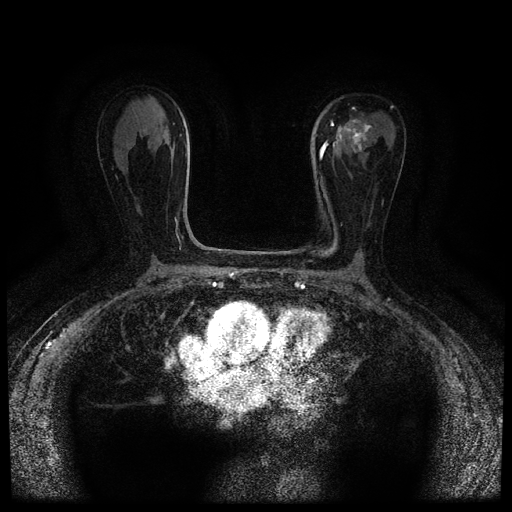
Breast MRI (dynamic contrast-enhanced, multi-phase), one axial slice. Position 45 of 116 along the scan axis. Dynamic contrast-enhanced series, time point 2 of 5 at this slice position (early post-contrast). 1.5 T. TE 2.7 ms, TR 5.4 ms. 2 mm slice thickness. 512 × 512 image matrix, field of view 320 × 320 mm. Female patient, age 80 years.
Annotated regions visible in this slice (semi-automatically segmented with operator editing):
- breast lesion (labelled 'tumour' in the annotation; benign lesions carry a separate 'benign' label): bounding box (x1, y1, x2, y2) in pixels: (333, 110, 372, 153)